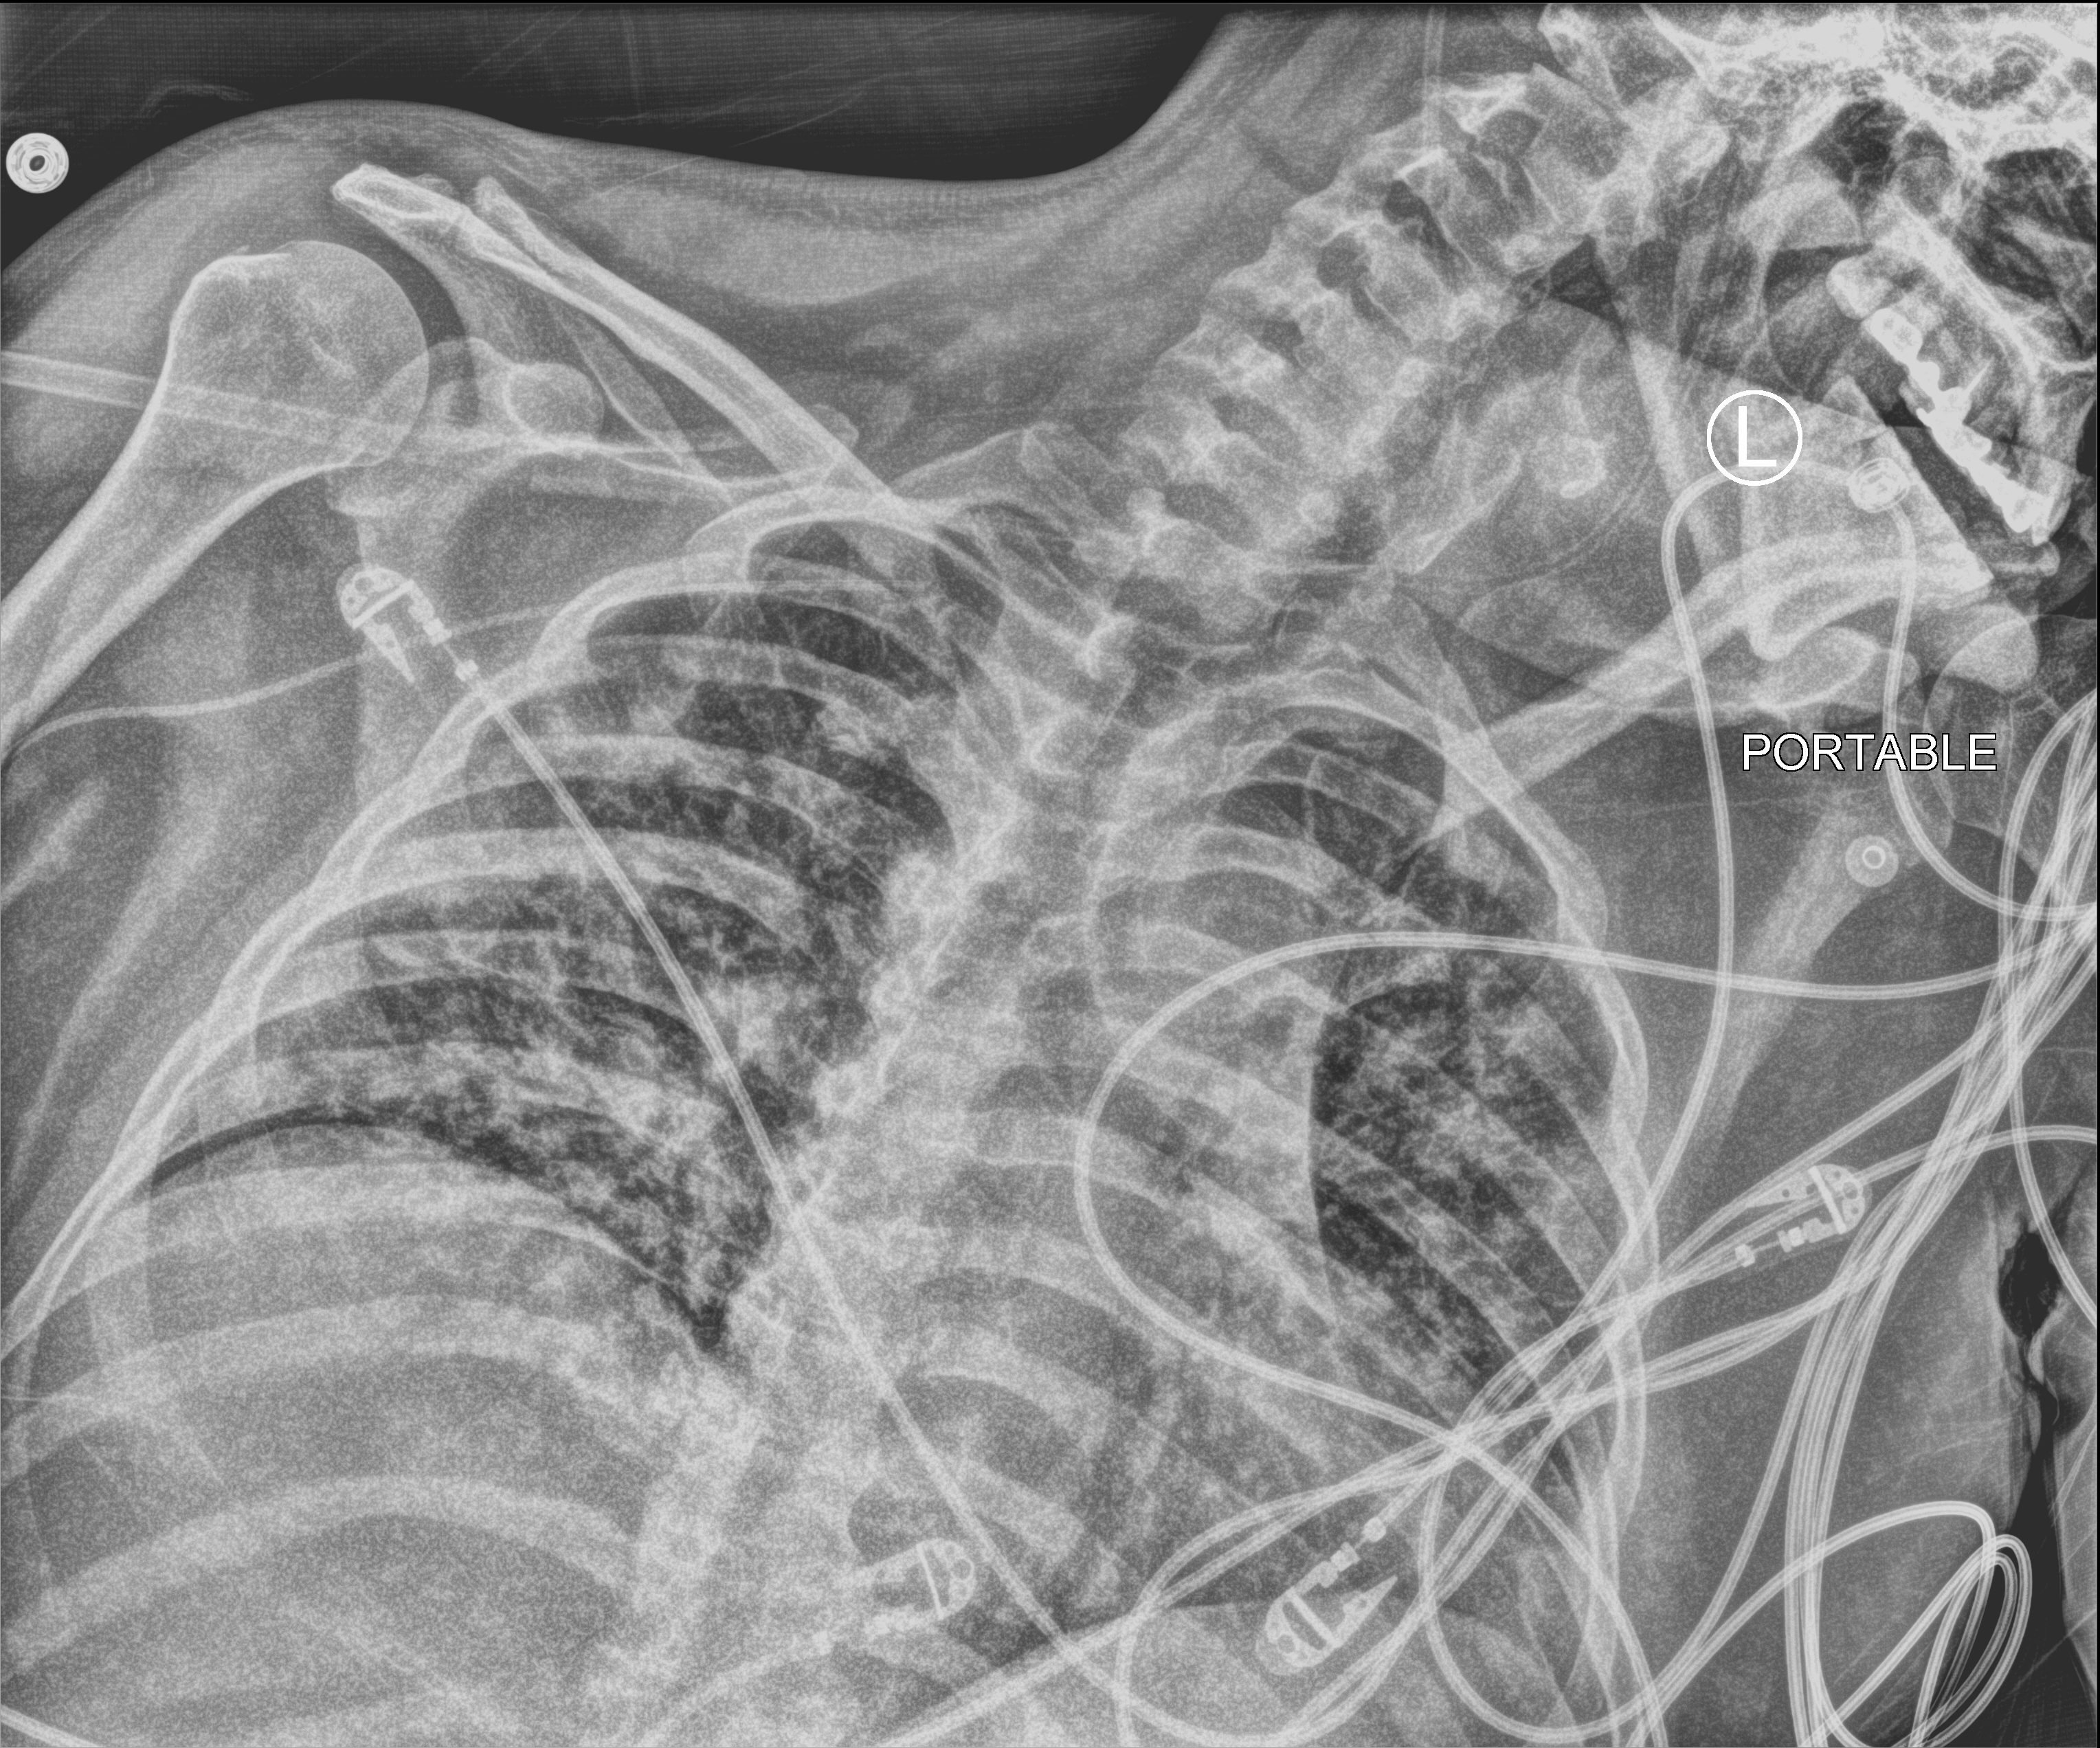
Portable chest radiograph; anteroposterior (AP) projection. Patient hospitalised with COVID-19; male, aged 18–59 years.
Admission-level facts for this patient (not findings on this image; timing relative to this image not recorded): hypertension (admission record): yes.